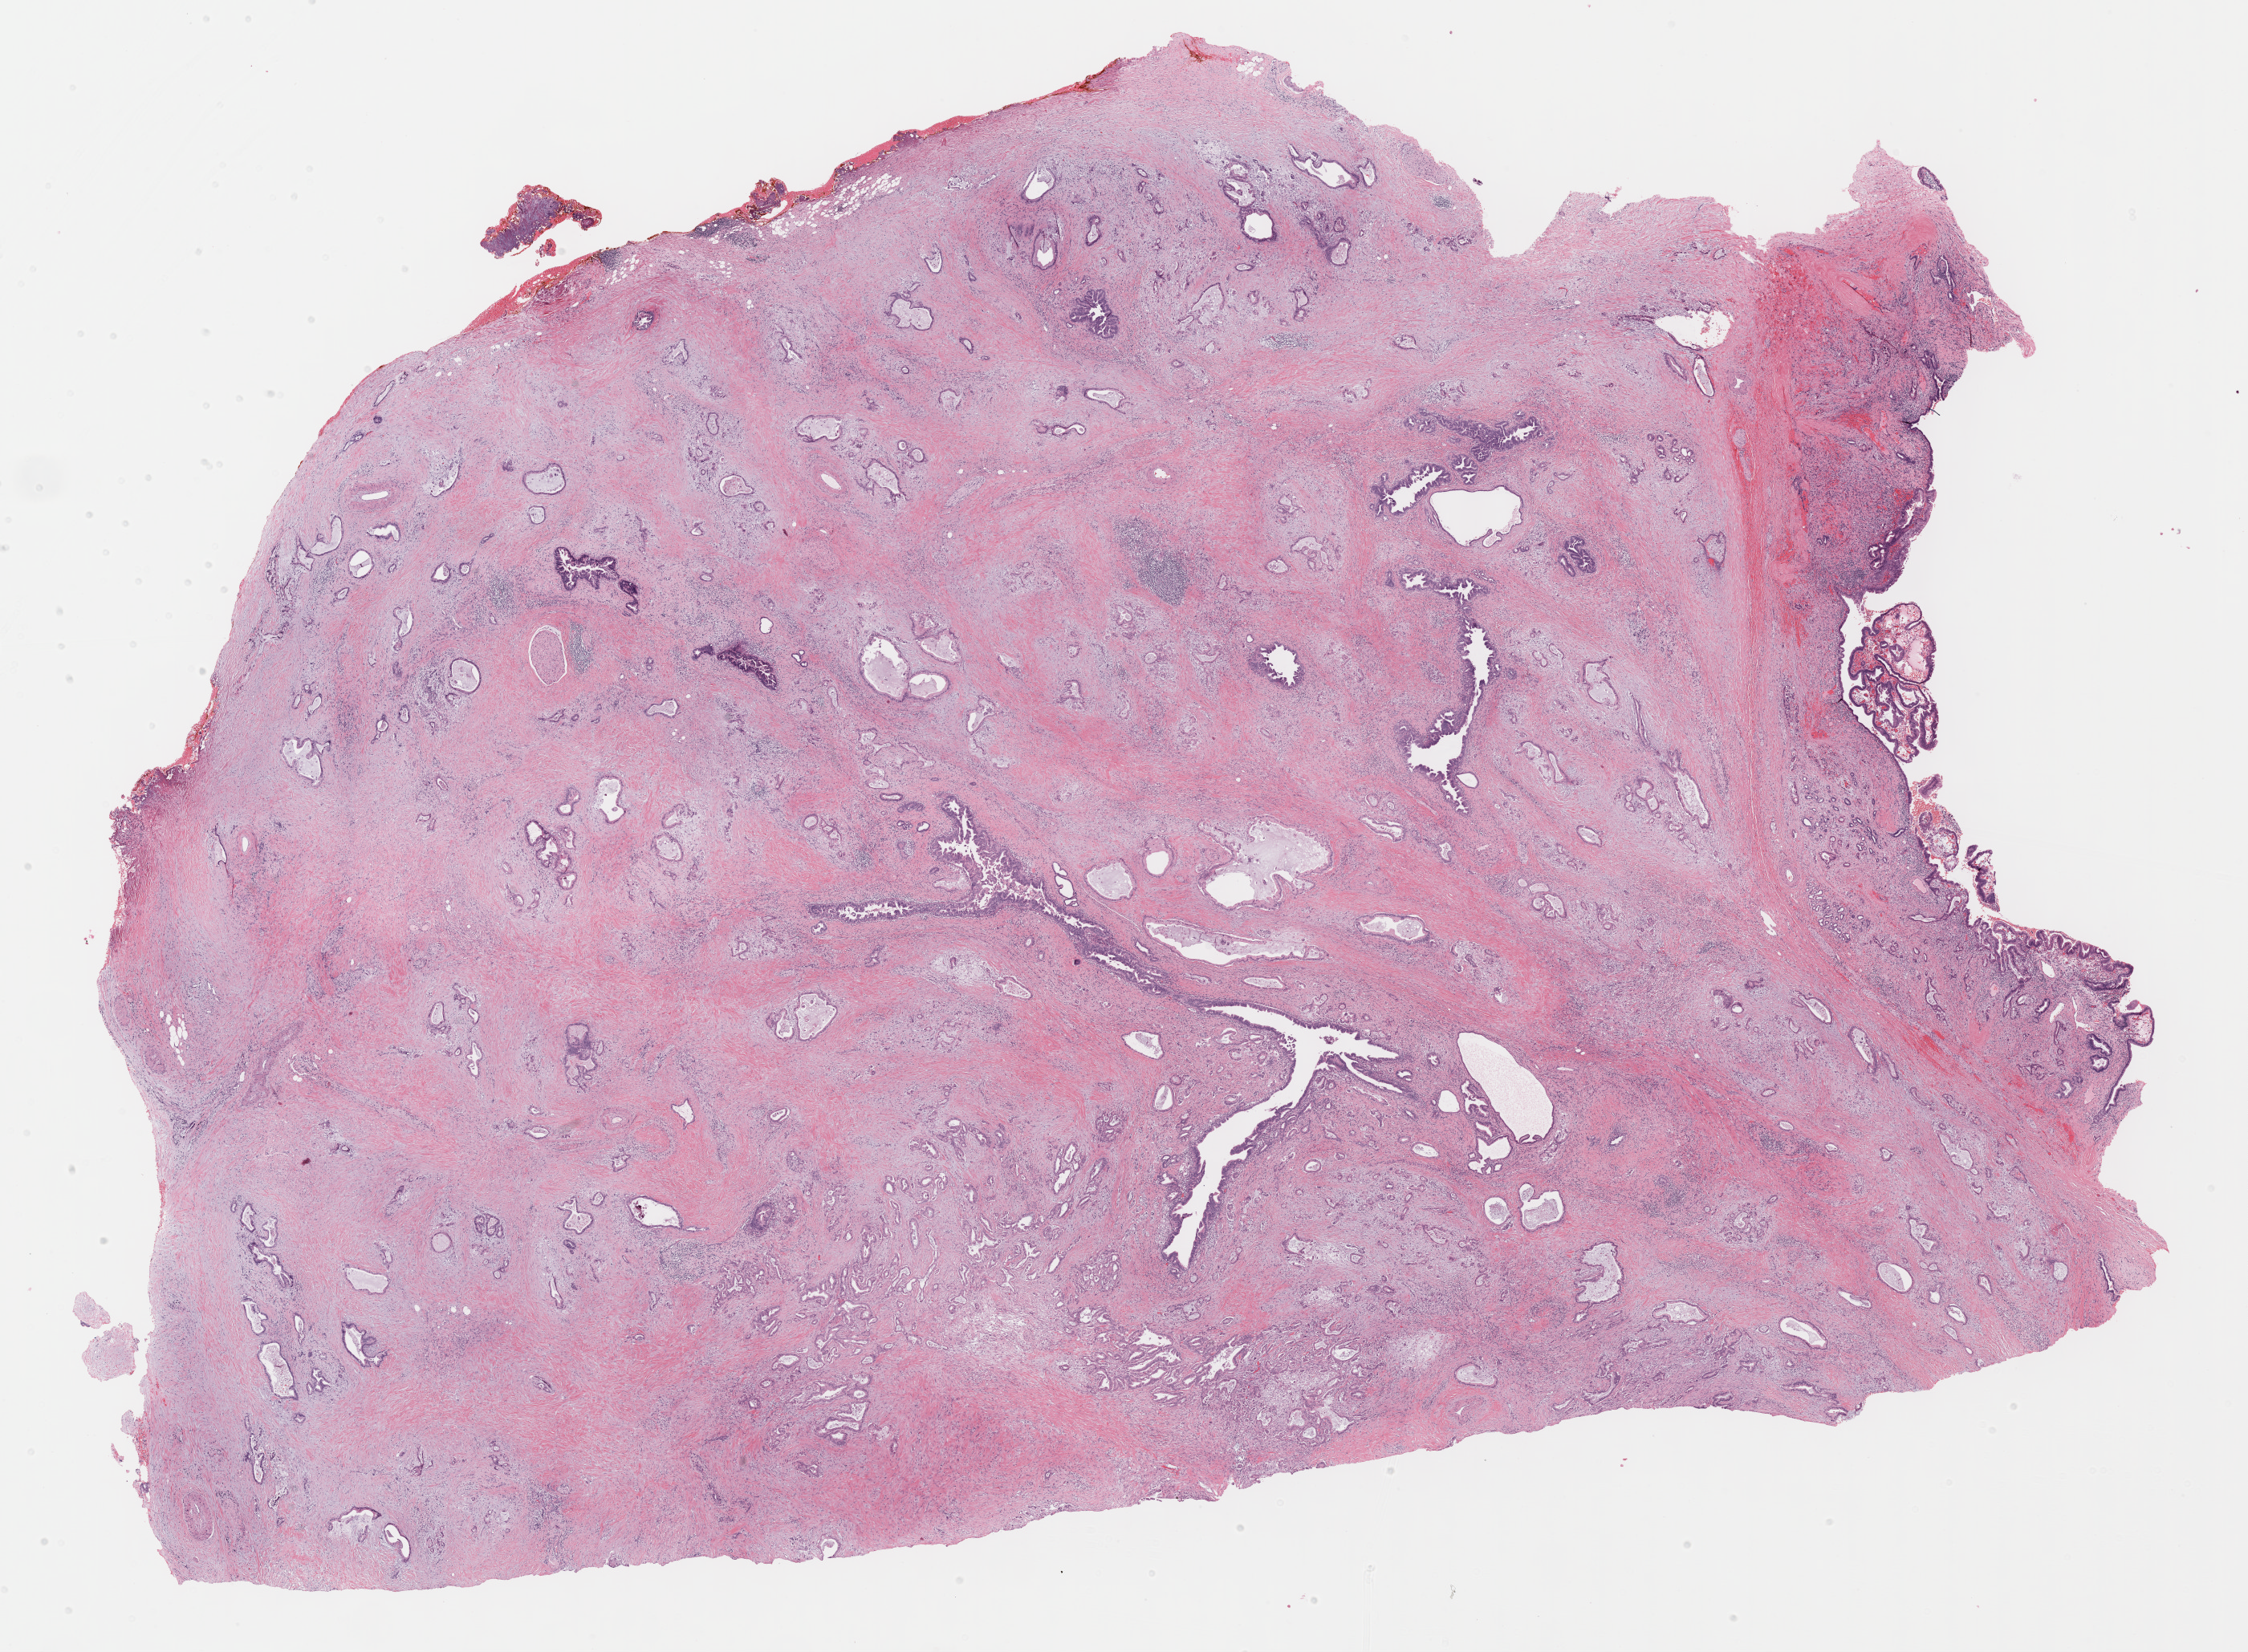
H&E-stained whole-slide image — low-resolution overview of the scanned area, about 22.7 x 16.7 mm. Formalin-fixed paraffin-embedded (FFPE) diagnostic section. Sample: primary tumour, pancreas. Male patient; age at initial diagnosis 71 years. Histologic grade: G2 (moderately differentiated).
TNM: T3 N1 M0. Histologic diagnosis: Infiltrating duct carcinoma, NOS (head of pancreas). AJCC pathologic stage: IIB (7th edition).